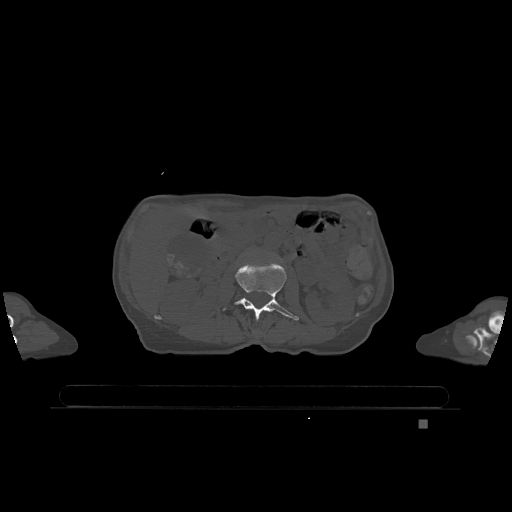
CT including the spine, one axial slice. Position 413 of 1317 along the scan axis. Bone window (W 1800 / L 400 HU). 0.5 mm slice thickness. 512 × 512 image matrix, field of view 500 × 500 mm. Patient: female, 74 years. From the clinical record (not read from this slice): primary cancer: lung; vertebrae with lytic lesions (as recorded): T1, T4, T5, T6, L4, L5.
Outlined on this slice (semi-automatically segmented with operator editing):
- L2 vertebra: bounding box [x1, y1, x2, y2] px = [218, 262, 299, 321]